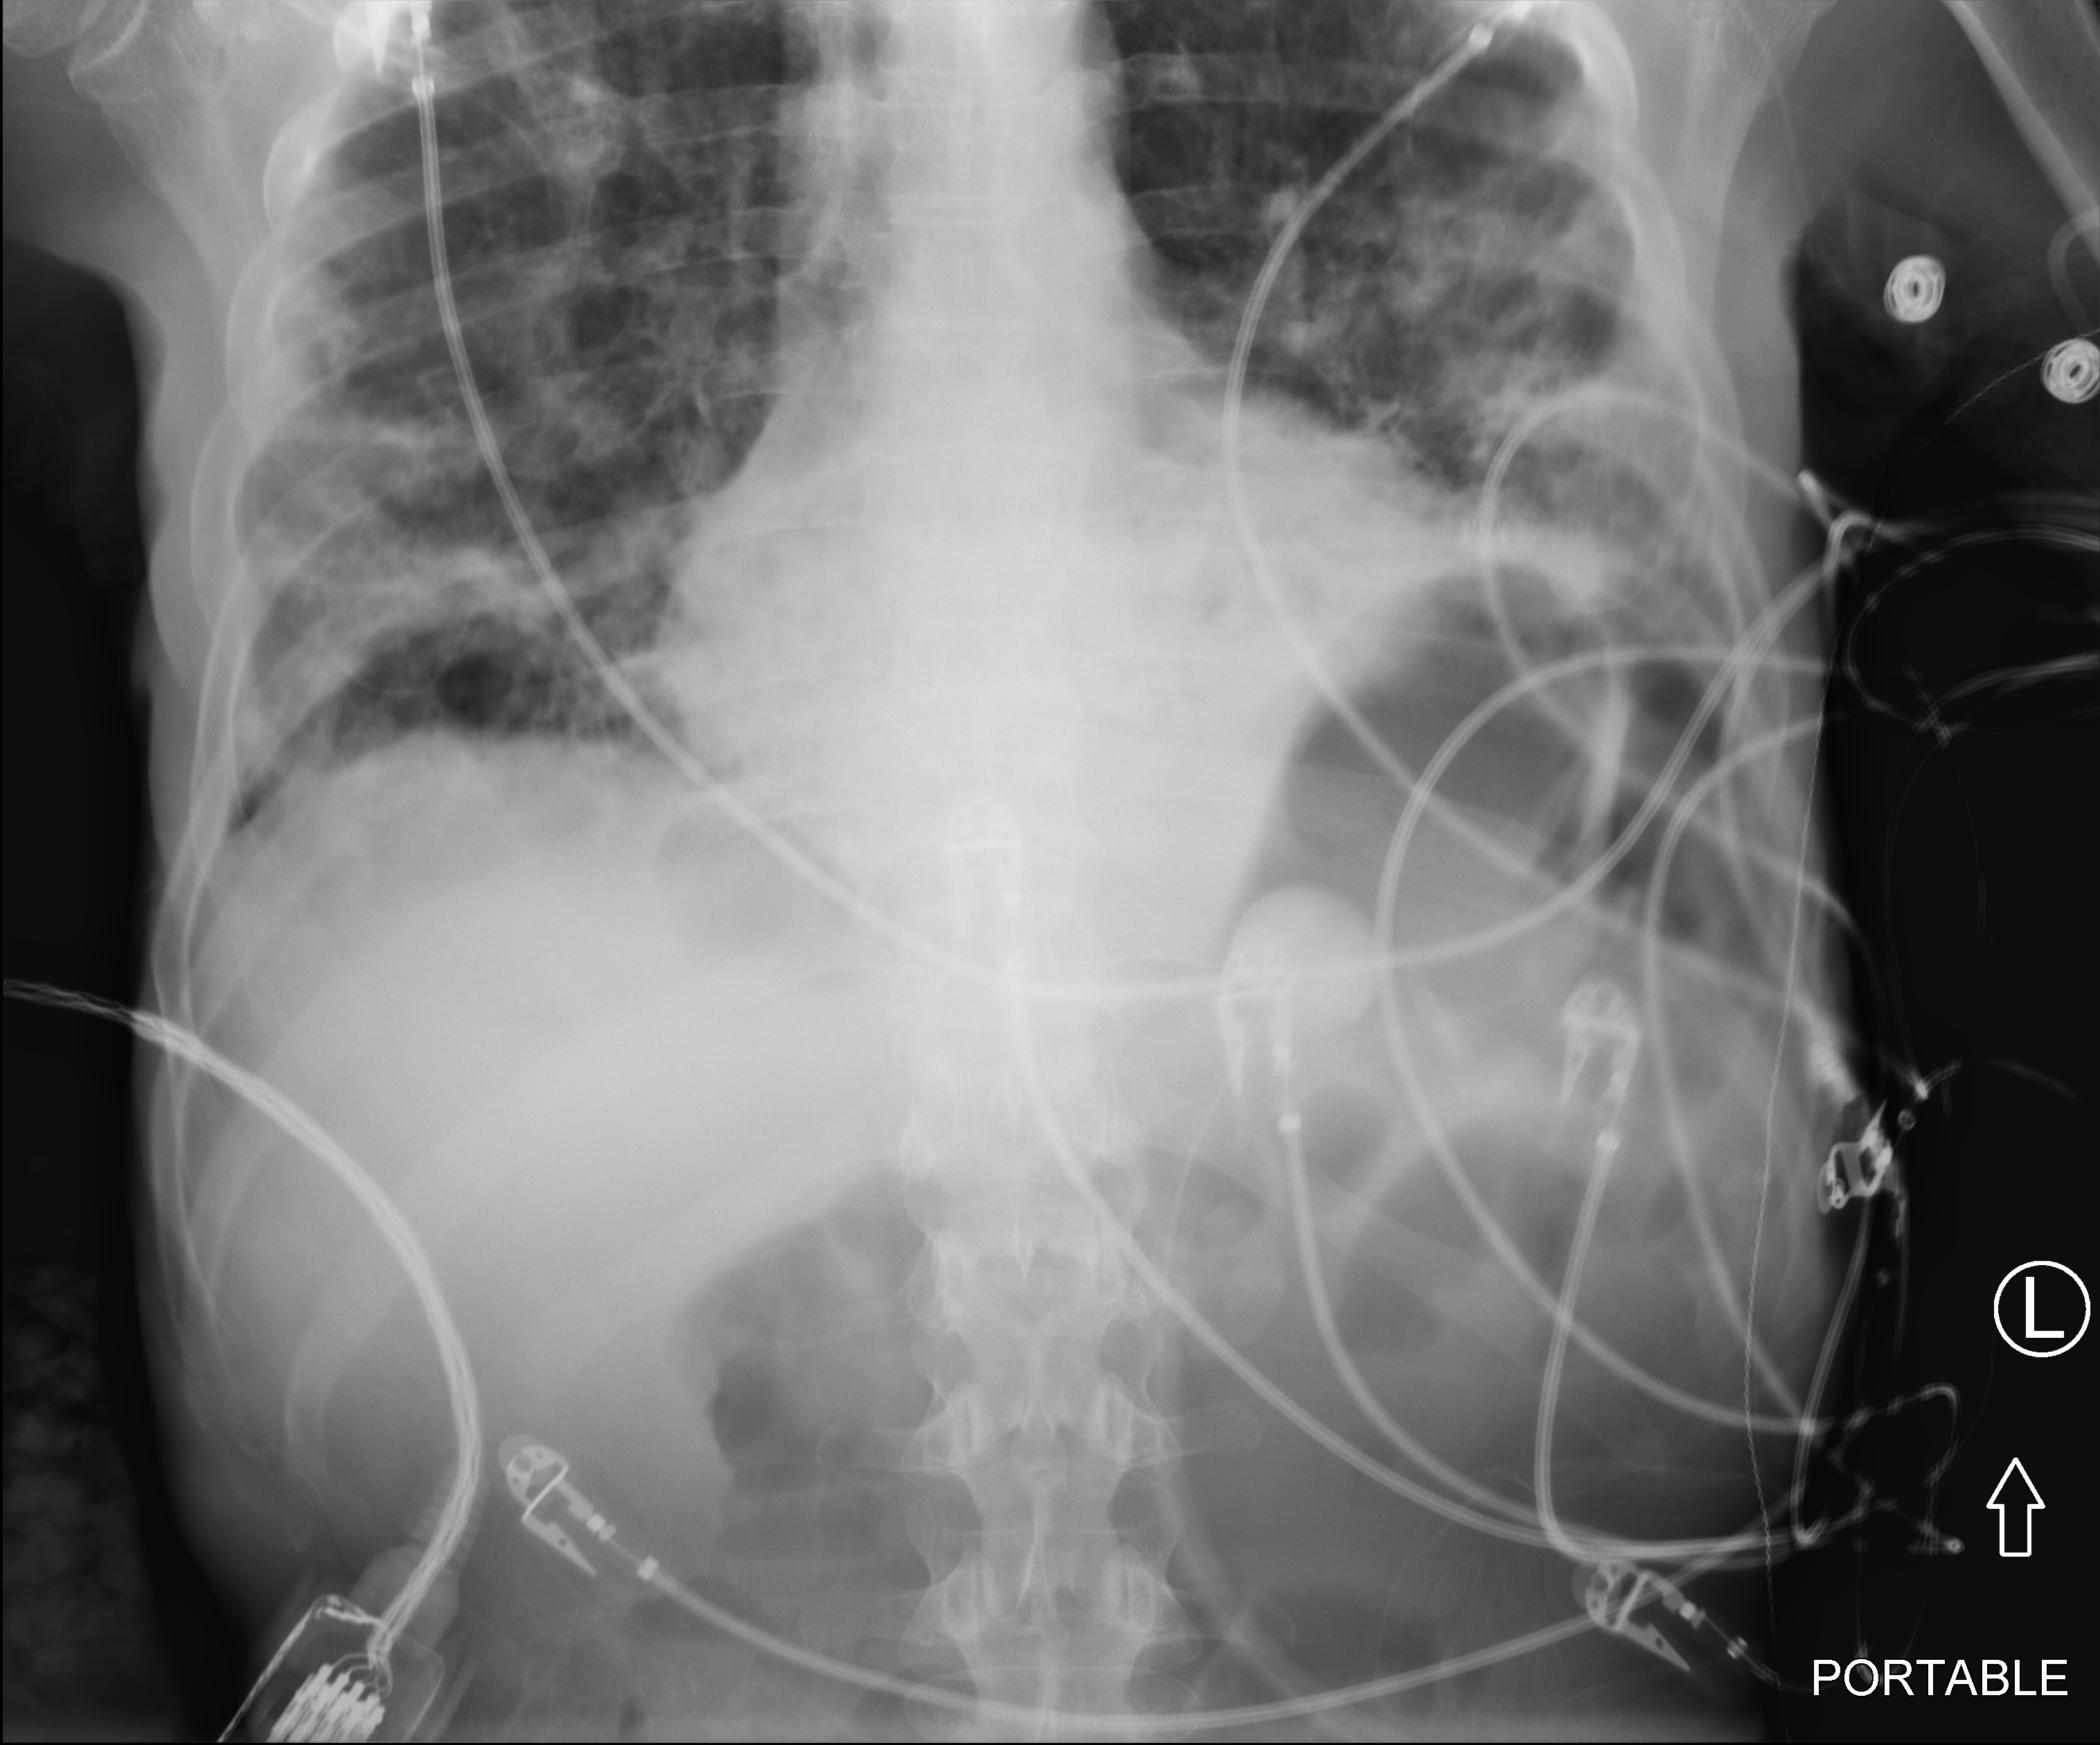
Bedside abdomen radiograph (computed radiography); anteroposterior (AP) projection. Patient hospitalised with COVID-19; male, aged 18–59 years.
From the hospital-stay record, not from the radiograph (when in the stay this image was taken is not recorded): hypertension (admission record): yes; admitted to intensive care during this hospital stay: yes; other chronic lung disease (admission record): no.